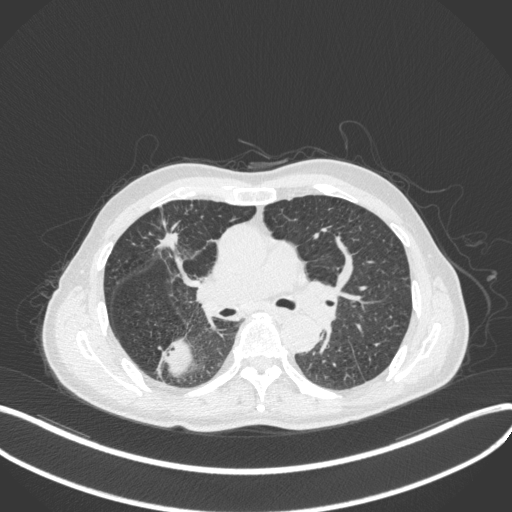
Chest CT, one axial slice; reconstruction kernel B31f; 120 kVp; lung window (W 1500 / L -600 HU); 512 × 512 image matrix, field of view 400 × 400 mm. Male patient, age 79 years. From the clinical record (not read from this slice): clinical TNM (as recorded): T3 N0 M0.
Structures marked on this image (bounding box drawn by a radiologist):
- lung tumour (recorded histology: adenocarcinoma): box from (x=156, y=335) to (x=194, y=379) px